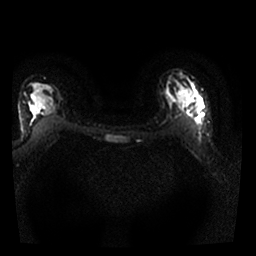
Breast MRI, one axial slice. Position 17 of 25 along the scan axis. Diffusion-weighted series; image 2 of 4 stored at this slice position (different b-values; order by instance number). 1.5 T. 256 × 256 image matrix. Female patient.
Outlined on this slice (expert manual segmentation):
- tumour on diffusion-weighted imaging: bounding box <186,104,206,125> (left, top, right, bottom; pixels)